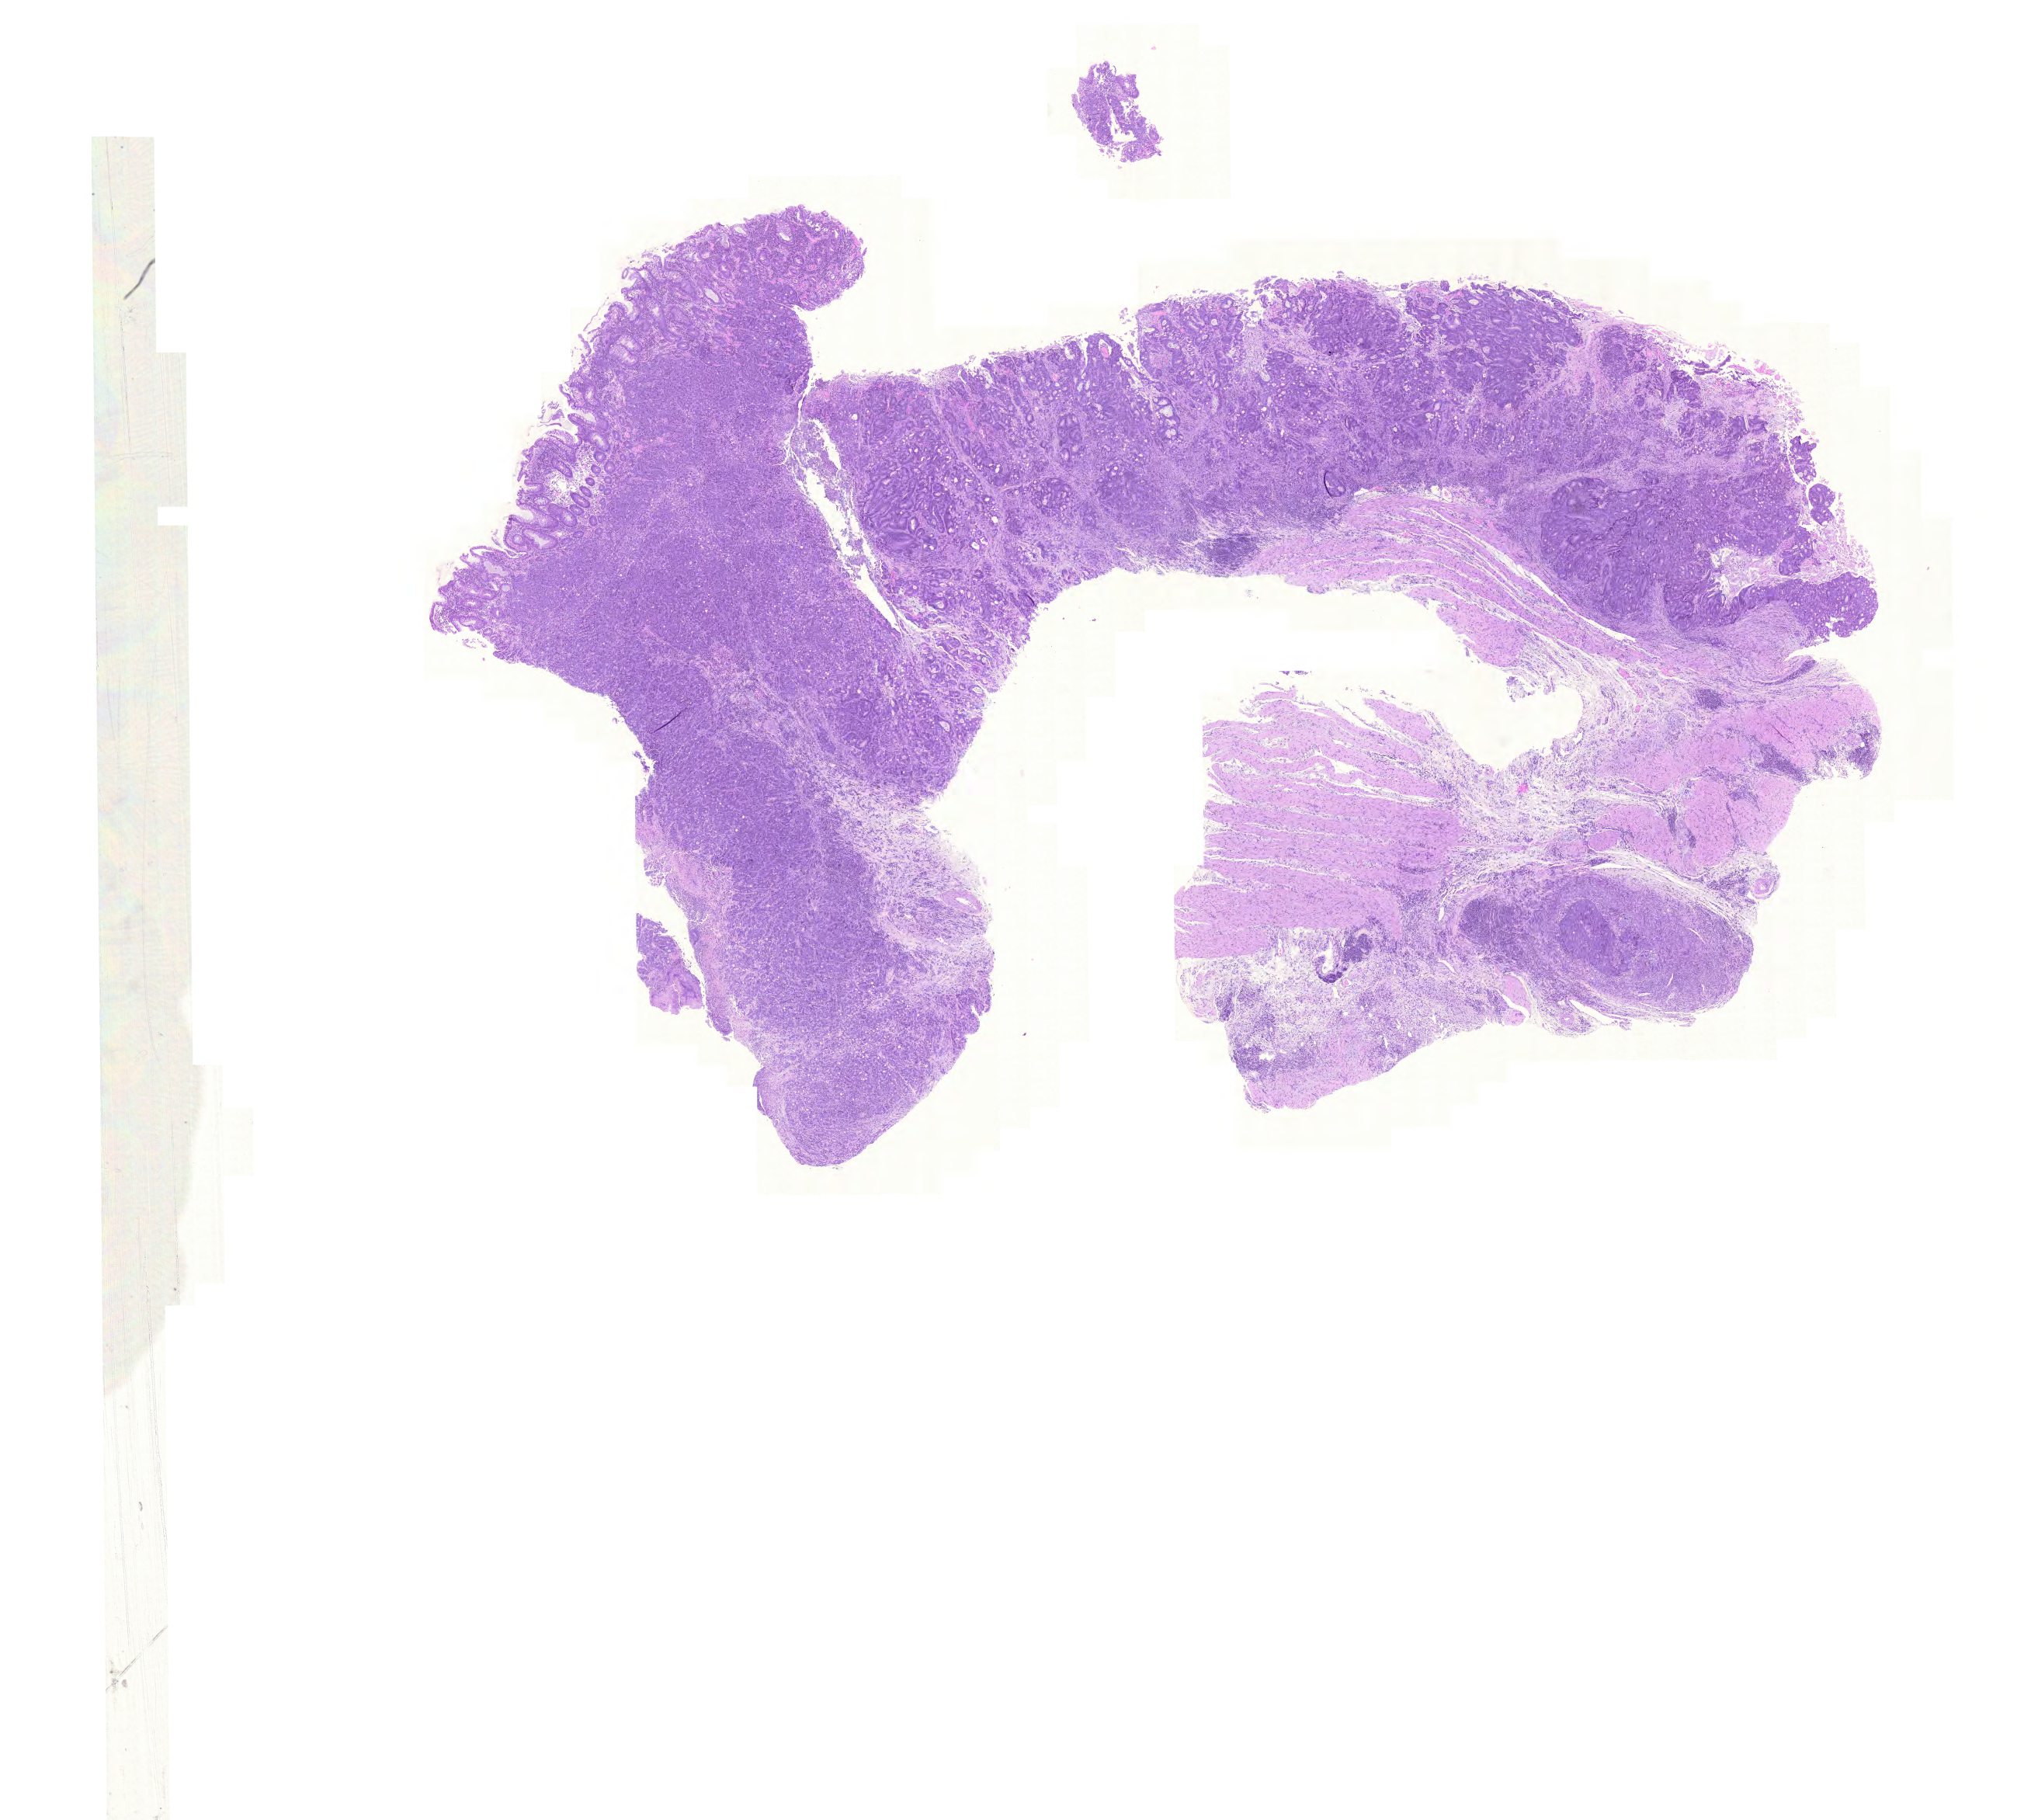
Digitized H&E-stained tissue section (whole slide), low-resolution overview of the scanned area, about 19.5 x 17.4 mm; formalin-fixed paraffin-embedded (FFPE) diagnostic section; colon, primary tumour sample. Female patient.
Pathologic diagnosis: Adenocarcinoma, NOS (transverse colon).